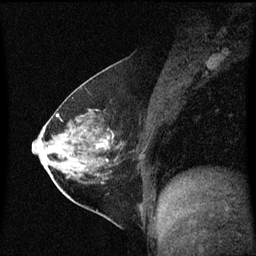
Breast MRI (dynamic contrast-enhanced), one sagittal slice; slice 26 of 60 in the series (ordered by position); dynamic contrast-enhanced series, image 2 of 3 at this slice position (ordered by acquisition); 1.5 T; TE 4.2 ms, TR 8.4 ms; 2 mm slice thickness; 256 × 256 image matrix. Female patient, age 54 years. From the clinical record (not read from this slice): setting: breast cancer imaged before/during neoadjuvant chemotherapy; receptor status: HER2-positive.
Annotated regions visible in this slice (semi-automatically segmented with operator editing):
- analysis volume of interest (the breast-tissue region the enhancement analysis was run in; not a lesion): box from (x=59, y=115) to (x=126, y=199) px
- tumour enhancement mask (voxels above the 70 % enhancement threshold inside the analysis volume of interest): (x=98, y=138)–(x=110, y=149)